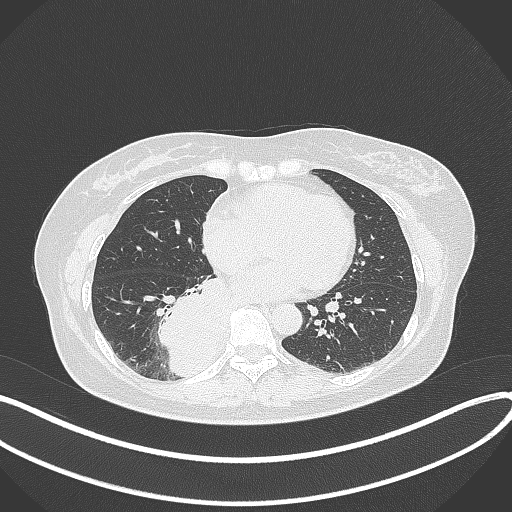
Chest CT, one axial slice; slice 142 of 331 in the series (ordered by position); reconstruction kernel B70f; lung window (W 1500 / L -600 HU); 512 × 512 image matrix, field of view 400 × 400 mm. Patient: female, 54 years. From the clinical record (not read from this slice): clinical TNM (as recorded): T4 N0 M0.
Annotated regions visible in this slice (bounding box drawn by a radiologist):
- lung tumour (recorded histology: adenocarcinoma): bounding box <154,271,237,378> (left, top, right, bottom; pixels)